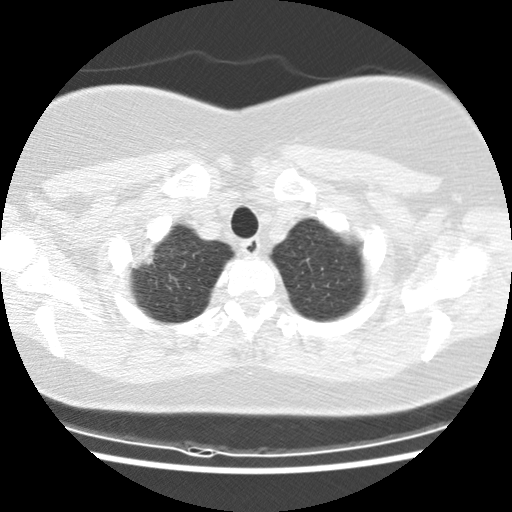
Low-dose screening chest CT, axial slice; baseline annual screen; lung window (W 1500 / L -600 HU); 120 kVp; slice 12 of 132 in the series. Female participant, aged 61 years at enrolment. Former smoker at enrolment.
• Expert reader's lesion annotation, box from (x=114, y=229) to (x=170, y=284) px.
• Reader record for this screening exam (exam-level; its link to the box is not recorded): non-calcified nodule or mass ≥4 mm, right upper lobe, 26 × 16 mm, spiculated (stellate) margins, mixed attenuation.
• Official screen result: positive, change unspecified: nodule(s) >= 4 mm or enlarging nodule(s), mass(es), or other non-specific abnormalities suspicious for lung cancer.
• Later outcome: lung cancer diagnosed 47 days after this screen — bronchiolo-alveolar carcinoma, mixed mucinous and non-mucinous, right upper lobe, well differentiated (G1), stage IA (AJCC 6th edition), 25 mm at pathology.